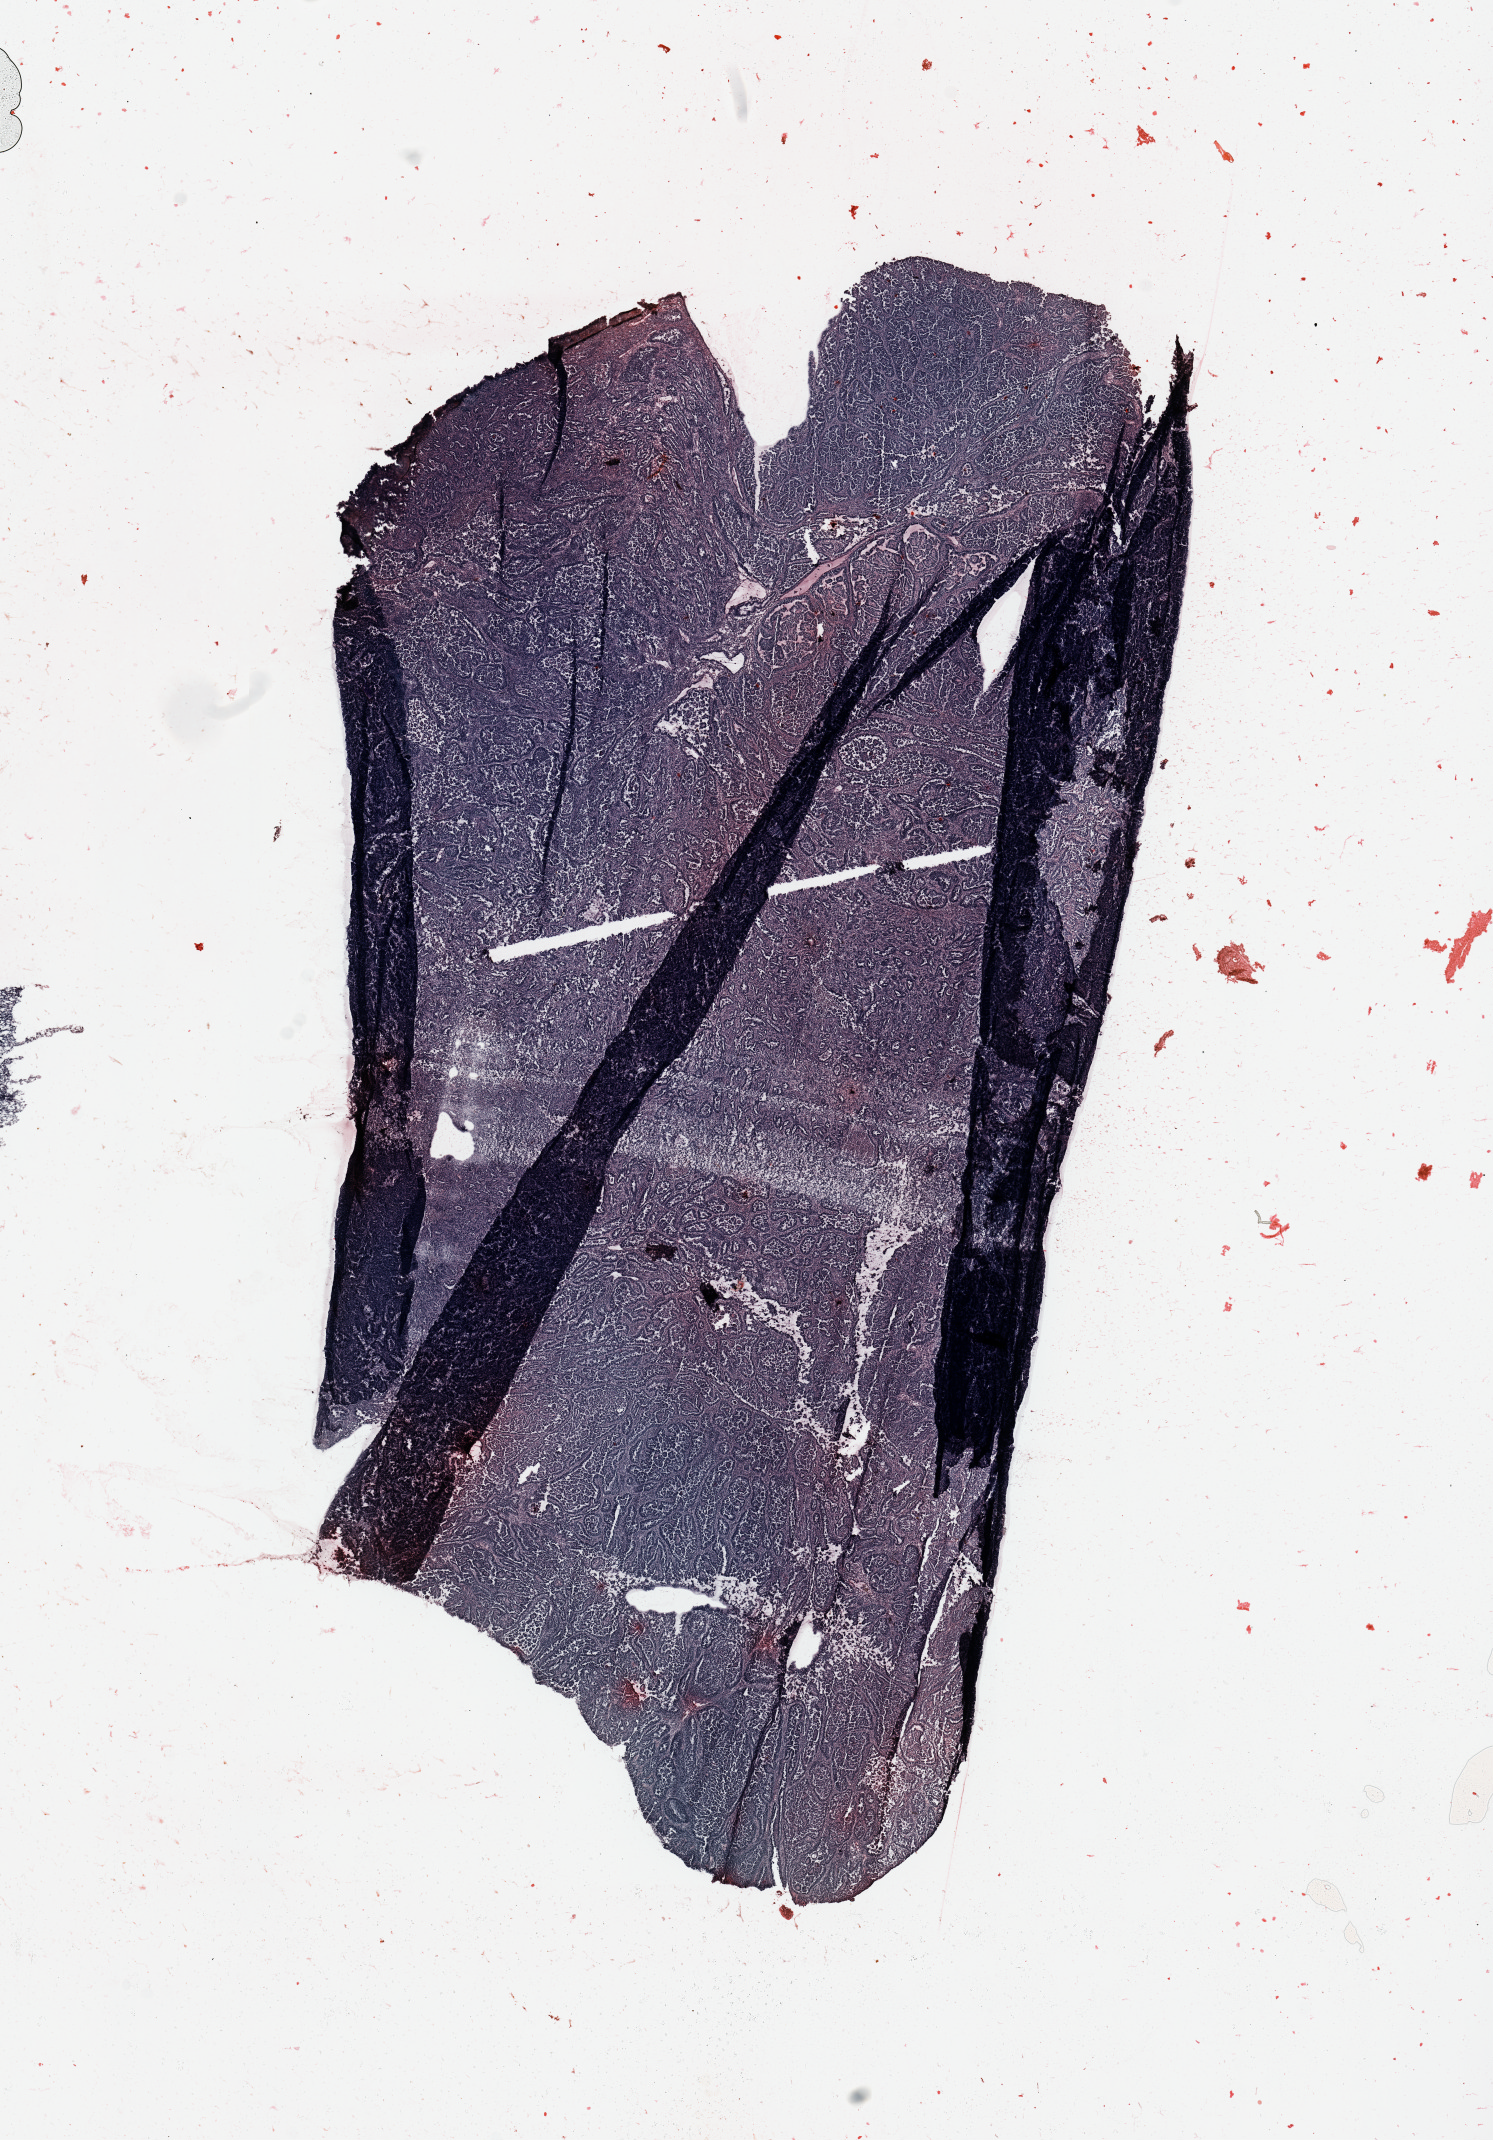
Whole-slide histology image, Hematoxylin and eosin (H&E) stained, low-resolution overview of the scanned area, about 11.8 x 16.9 mm (slide scanned at 20x). Tumour tissue sample, uterus. Female, 60 y/o. Histologic grade: G3 (poorly differentiated).
AJCC pathologic stage: III. Diagnosis: Endometrioid adenocarcinoma, NOS.